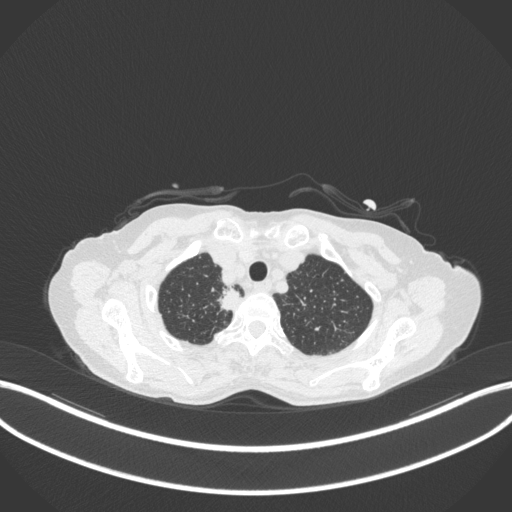
Chest CT, one axial slice. Slice 327 of 363 in the series (ordered by position). Lung window (W 1500 / L -600 HU). 1 mm slice thickness. 512 × 512 image matrix, field of view 400 × 400 mm. Patient: female, 75 years. Case-level facts recorded for this patient, not image findings: clinical TNM (as recorded): T1c N1 M1.
Structures marked on this image (bounding box drawn by a radiologist):
- lung tumour (recorded histology: adenocarcinoma): bounding box [x1, y1, x2, y2] px = [213, 286, 248, 314]